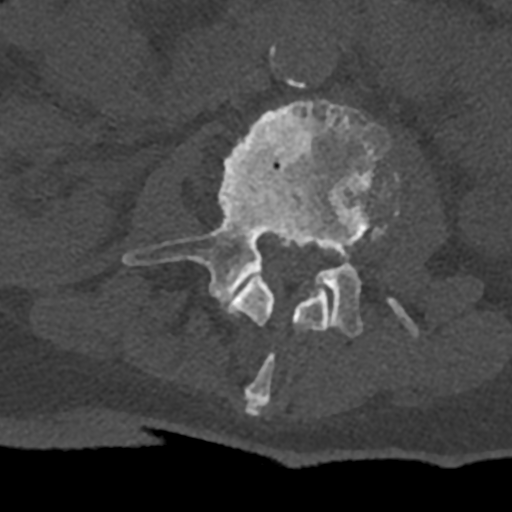
CT including the spine, one axial slice; slice 341 of 797 in the series (ordered by position); reconstruction kernel Br40s/3; bone window (W 1800 / L 400 HU); 512 × 512 image matrix, field of view 160 × 160 mm. Male patient, age 74 years. From the clinical record (not read from this slice): primary cancer: renal.
Outlined on this slice (semi-automatically segmented with operator editing):
- L2 vertebra: bounding box <227,268,330,416> (left, top, right, bottom; pixels)
- L3 vertebra: <123,99,418,338>